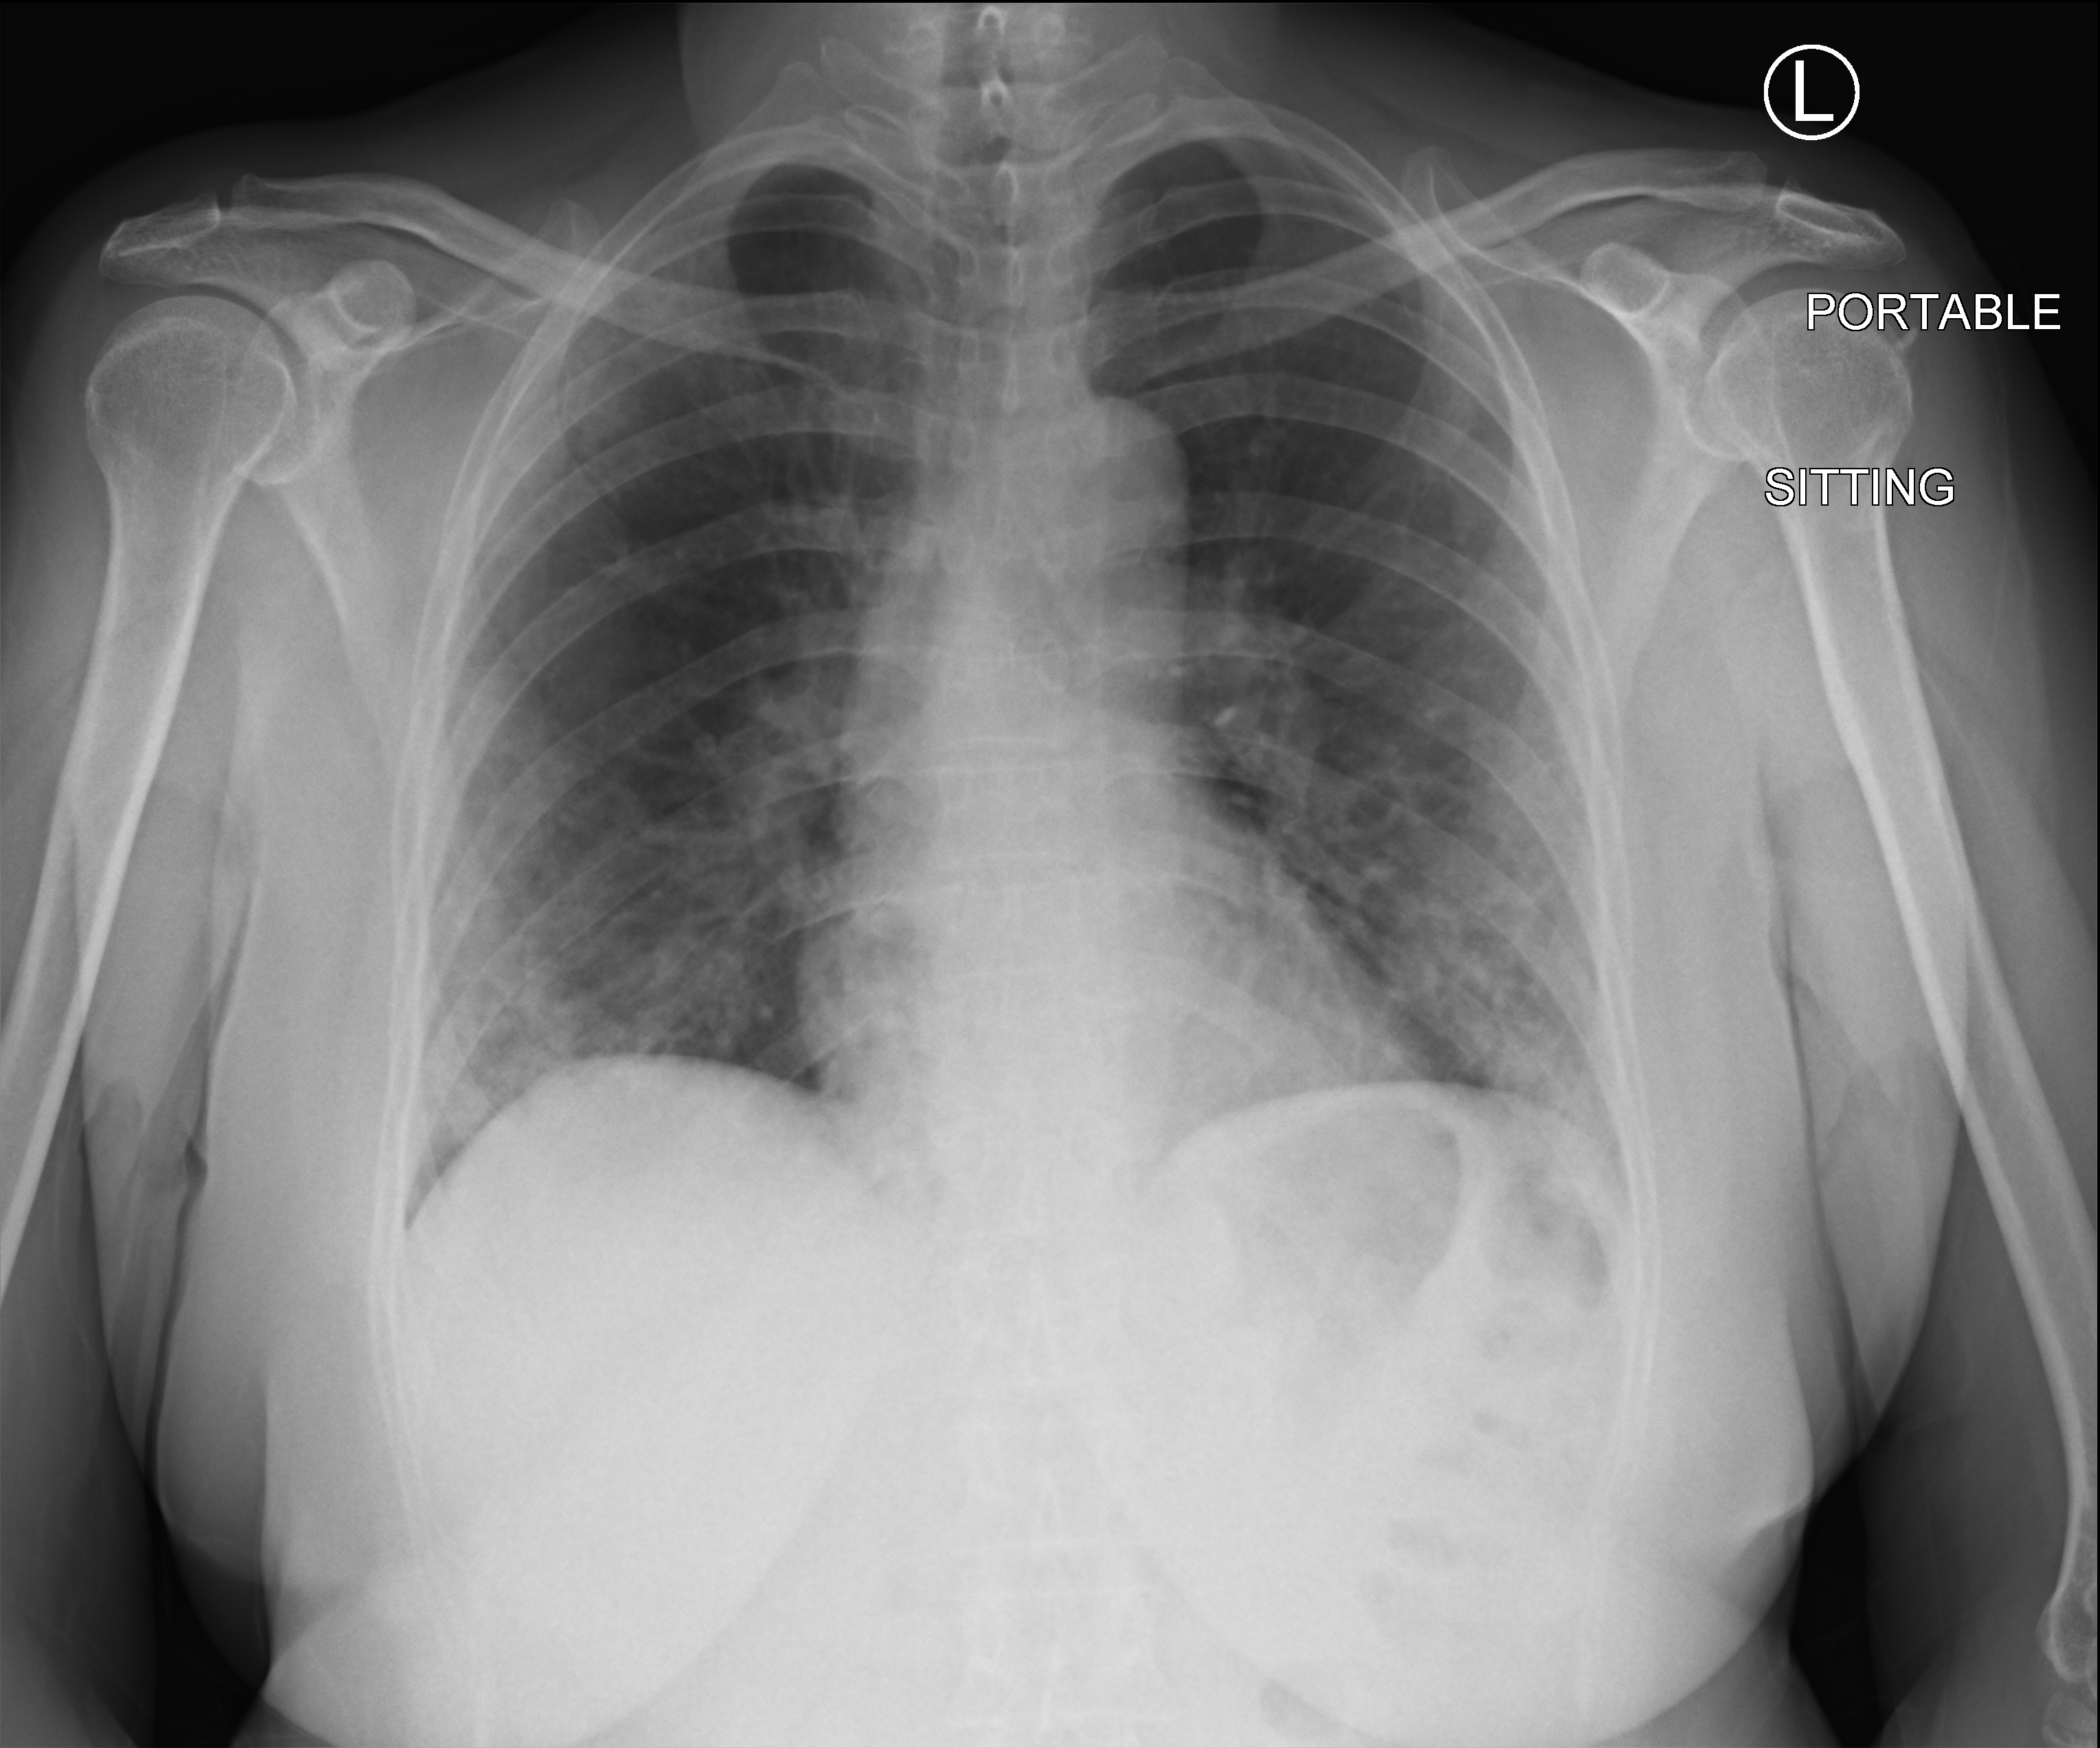
Bedside chest radiograph (computed radiography); anteroposterior (AP) projection. Patient hospitalised with COVID-19; female, aged 18–59 years.
Admission-level facts for this patient (not findings on this image; timing relative to this image not recorded):
- admitted to intensive care during this hospital stay: no